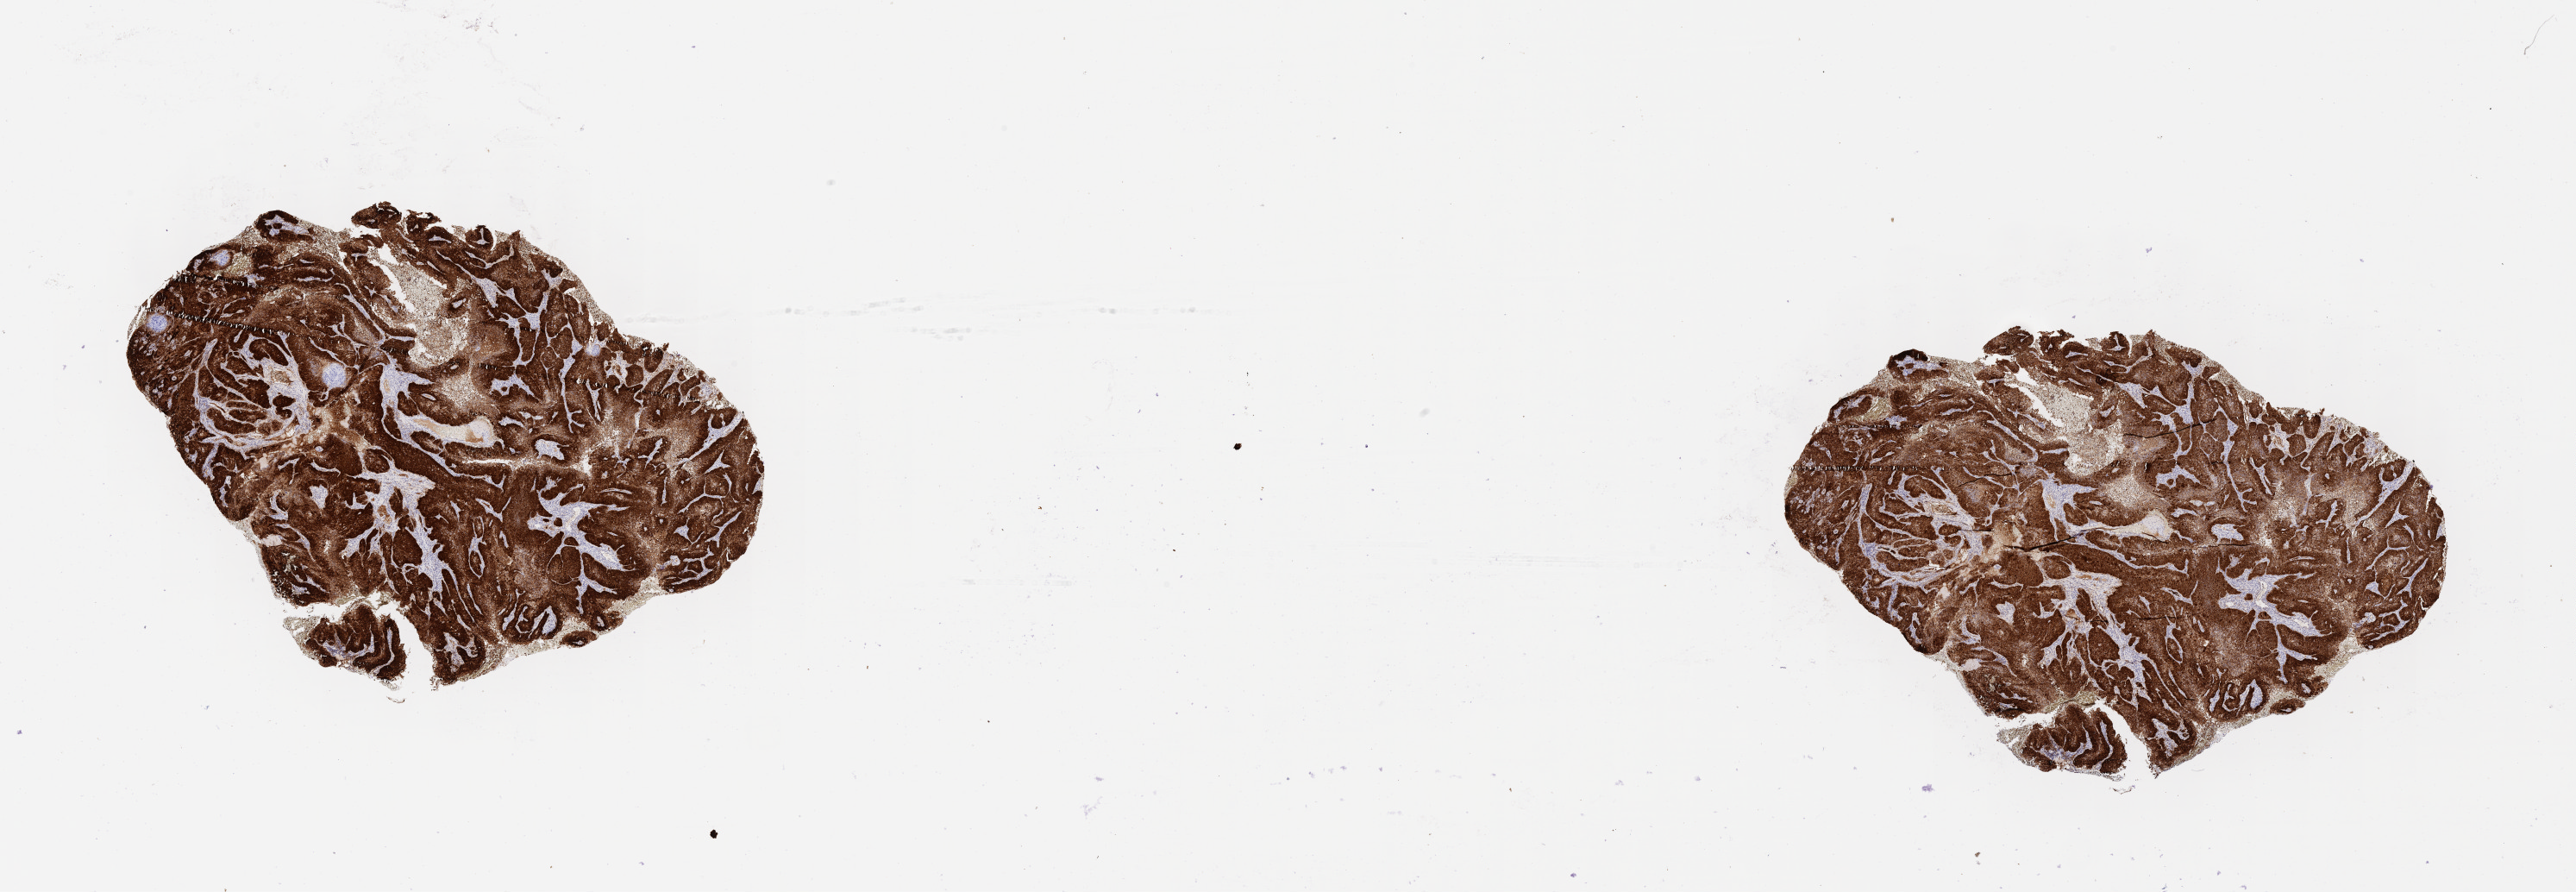
IHC for p16 (p16INK4a), whole-slide image — a low-resolution overview of the entire scanned area, about 24.2 x 8.4 mm; specimen: tumor tissue; site: cervix. Patient female; age 40 years.
* histologic diagnosis: Squamous cell carcinoma, large cell, nonkeratinizing, NOS